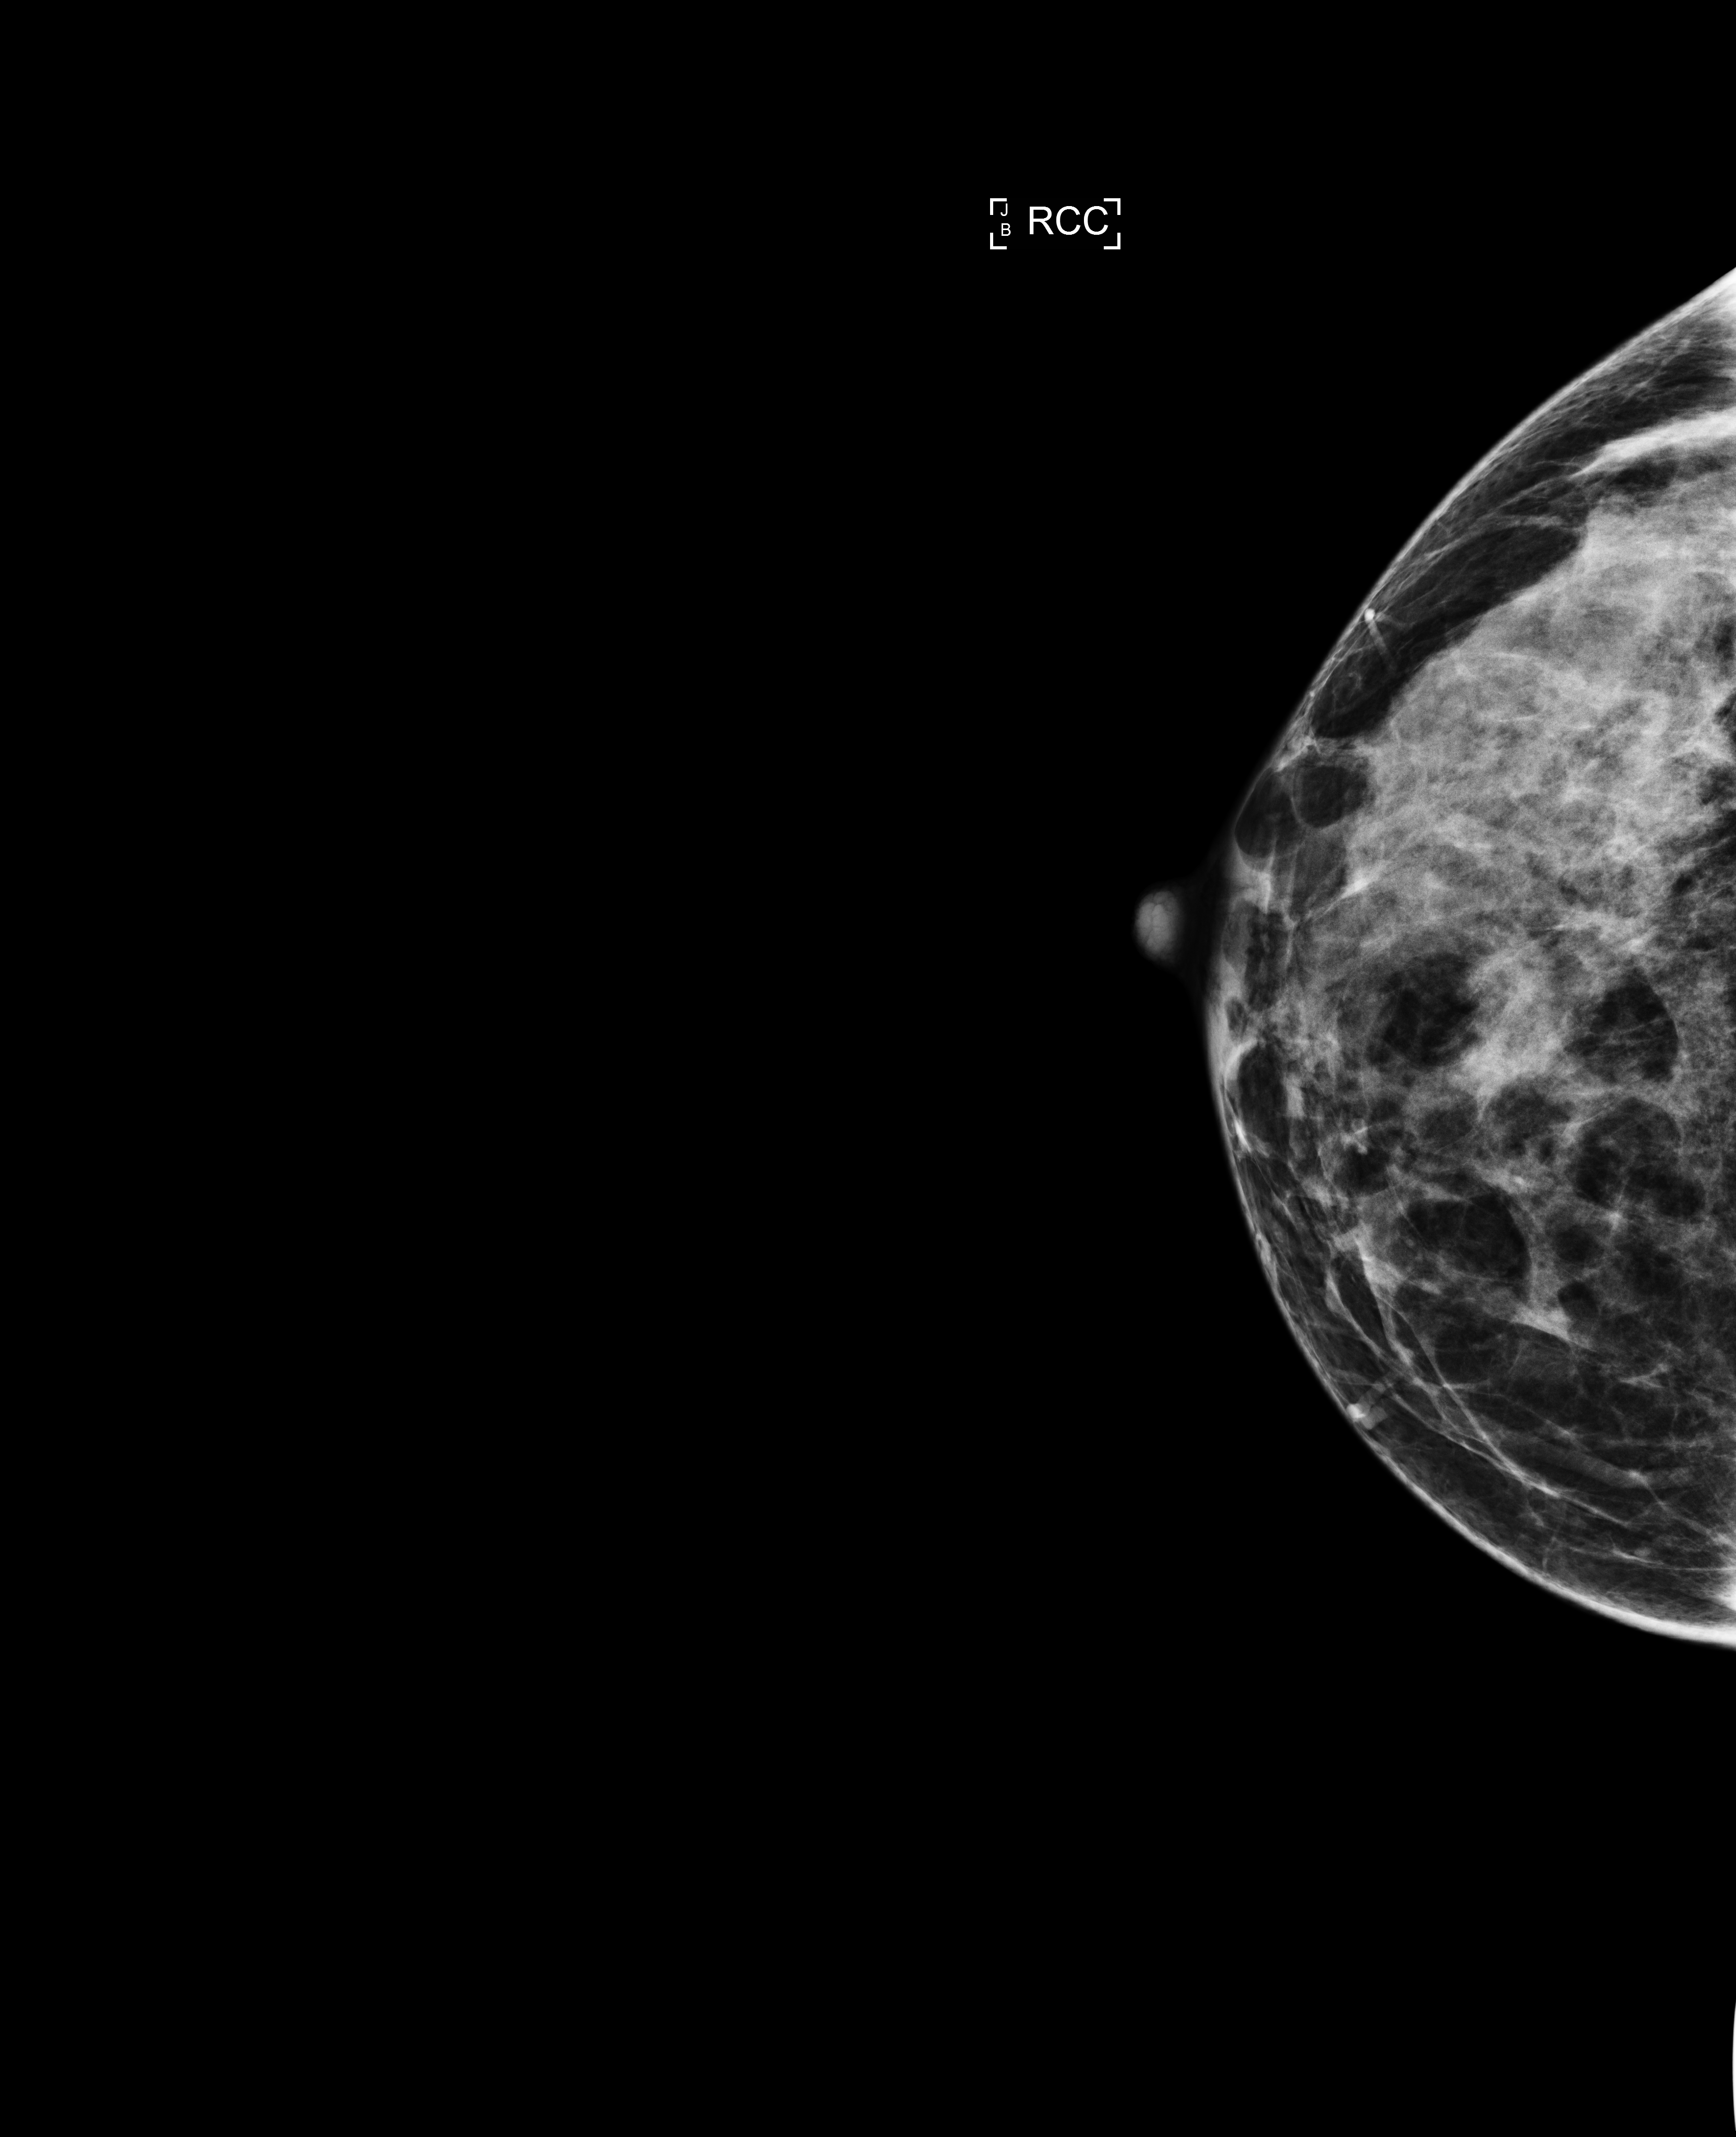
Screening examination. Female patient, age 42 years.
Image type: full-field digital mammogram. Breast: right. Projection: cranio-caudal projection.